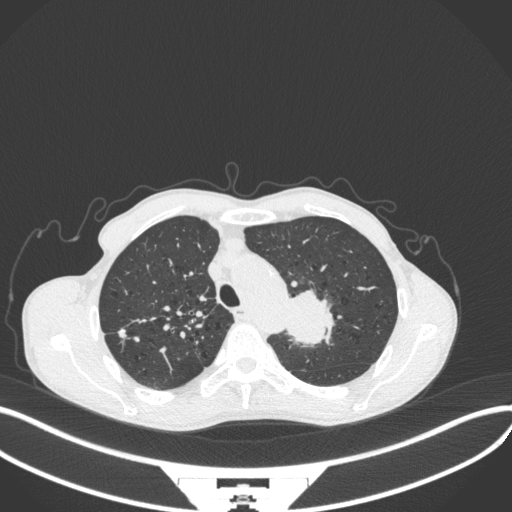
Chest CT, one axial slice; position 322 of 394 along the scan axis; lung window (W 1500 / L -600 HU); 1 mm slice thickness; 512 × 512 image matrix, field of view 400 × 400 mm. Patient: male, 65 years. From the clinical record (not read from this slice): clinical TNM (as recorded): T2b N0 M0.
Outlined on this slice (rectangle marked by the reading radiologist):
- lung tumour (recorded histology: adenocarcinoma): bounding box <279,285,337,351> (left, top, right, bottom; pixels)